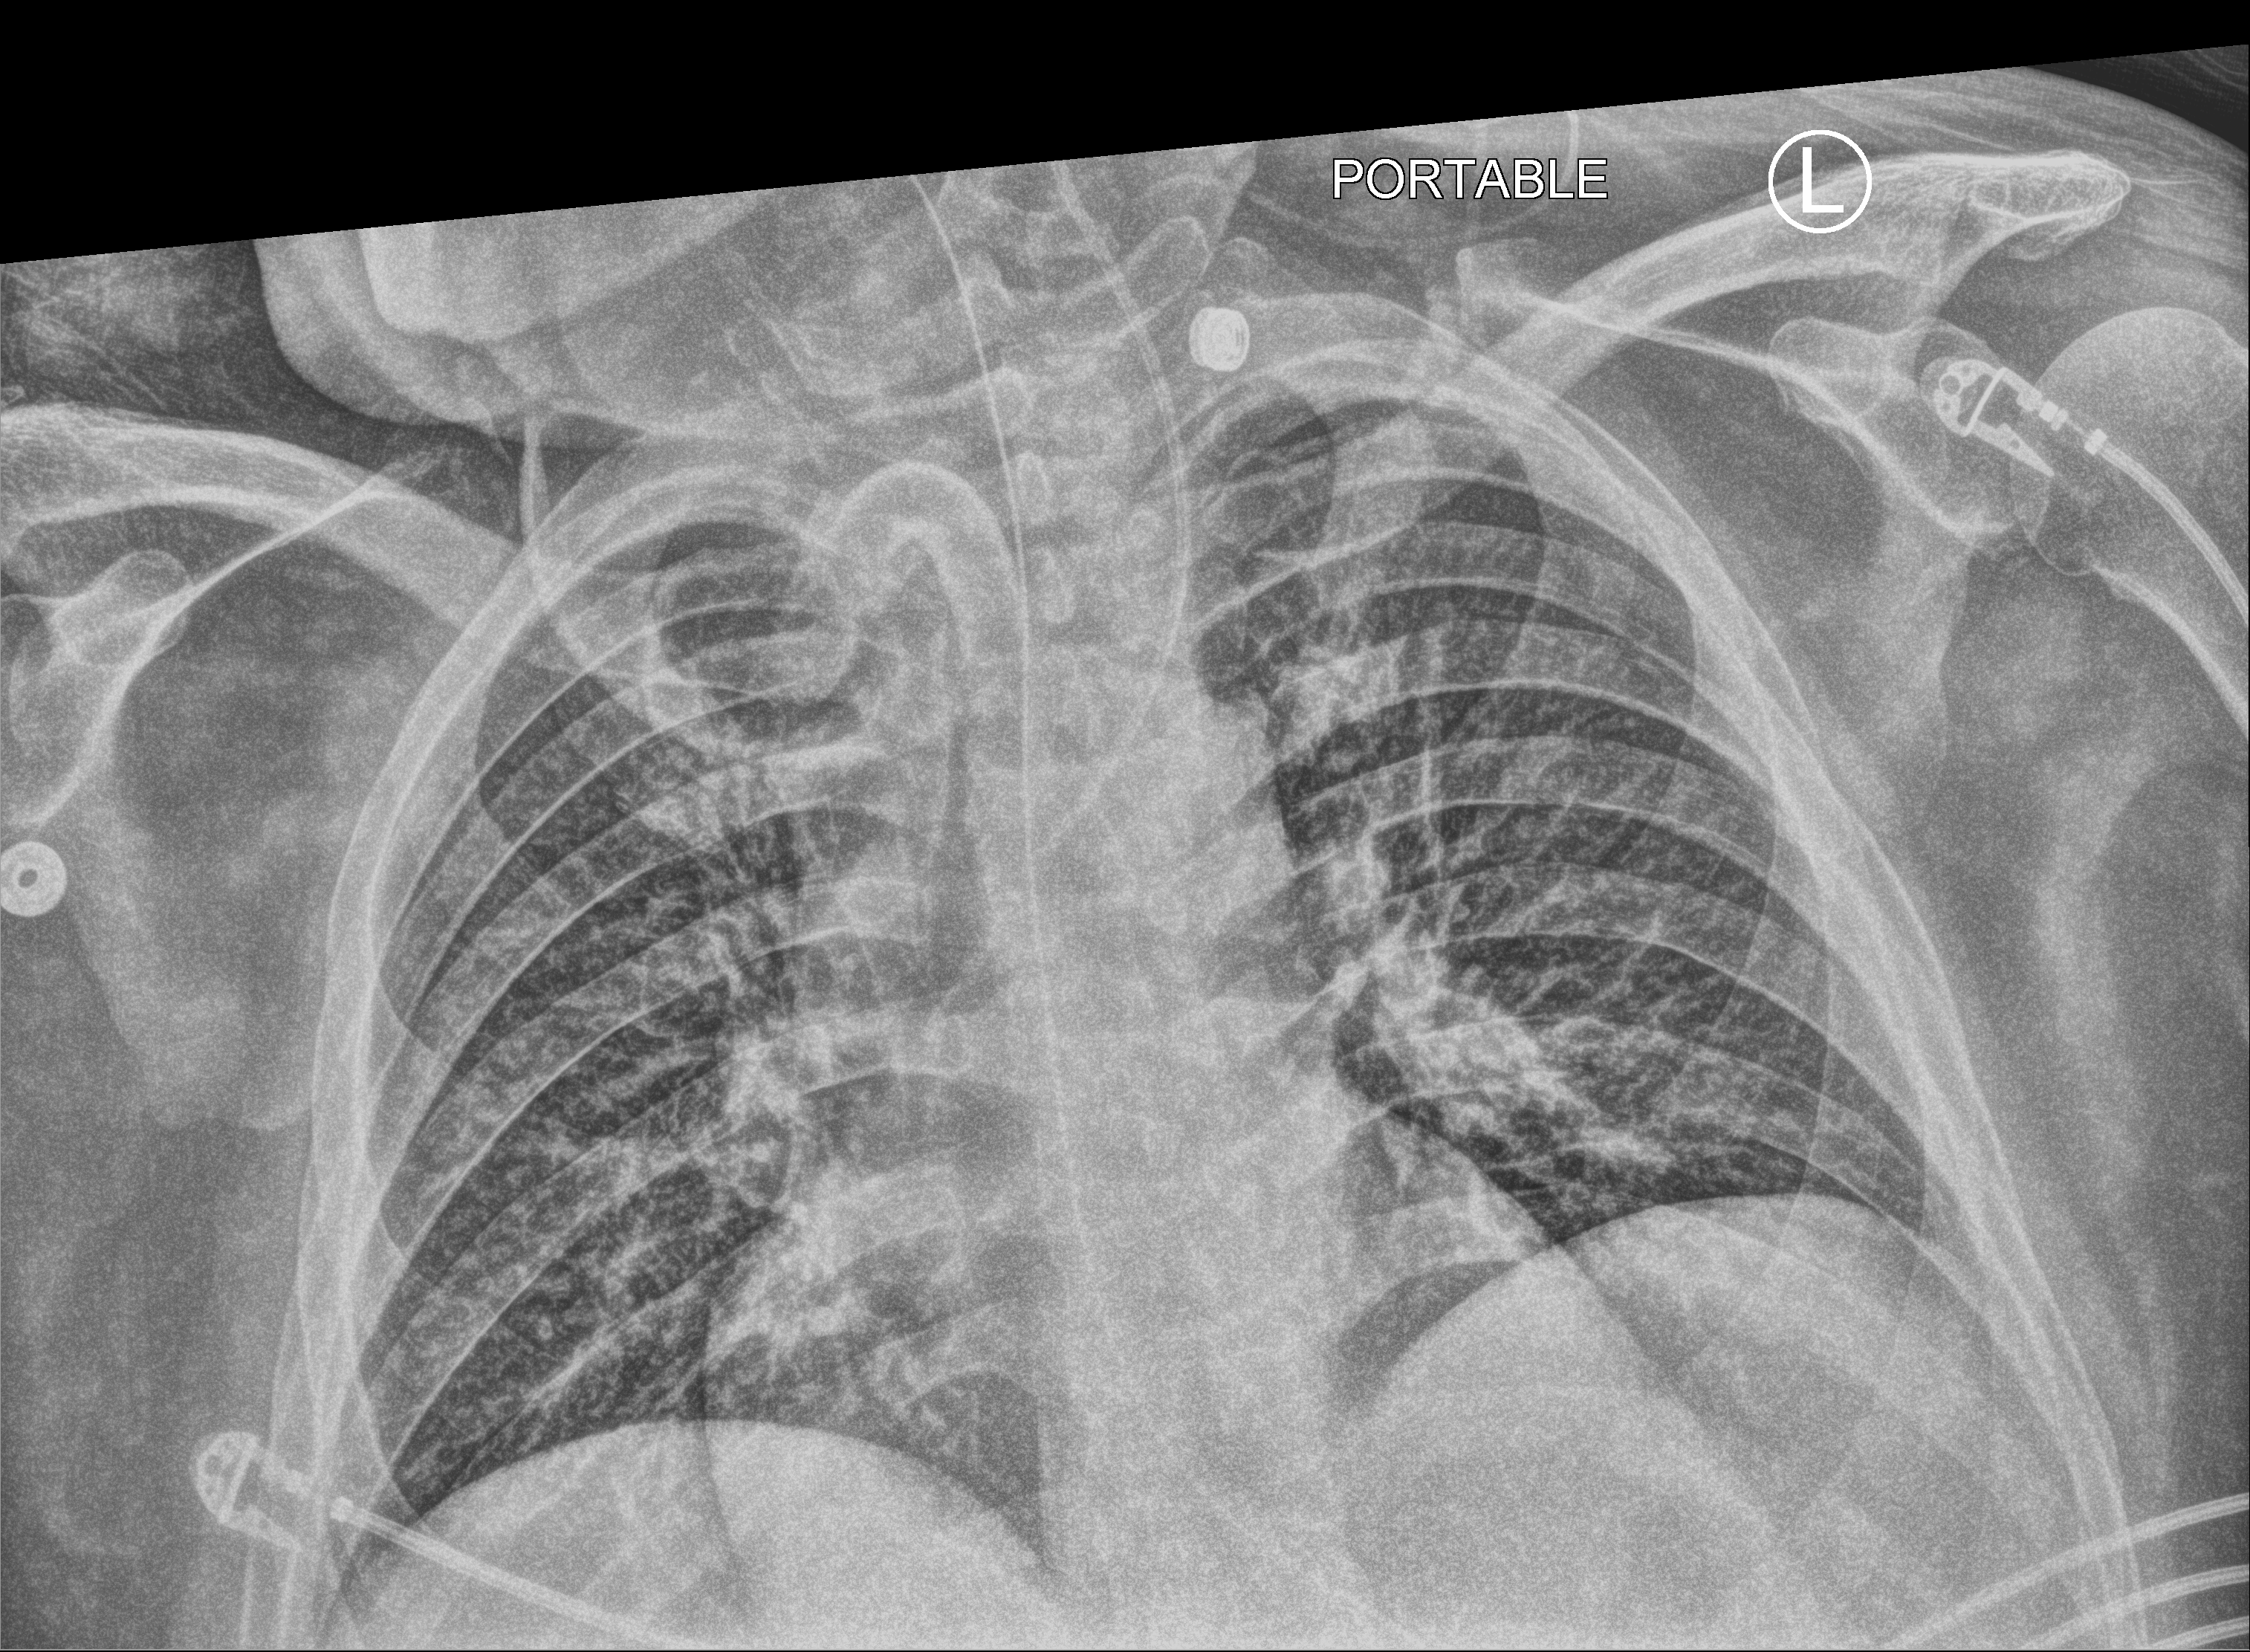
Chest X-ray (portable), anteroposterior (AP) projection. Male patient hospitalised with COVID-19, age 18–59 years.
Admission-level facts for this patient (not findings on this image; timing relative to this image not recorded):
- admitted to intensive care during this hospital stay: yes
- mechanically ventilated during this hospital stay: yes